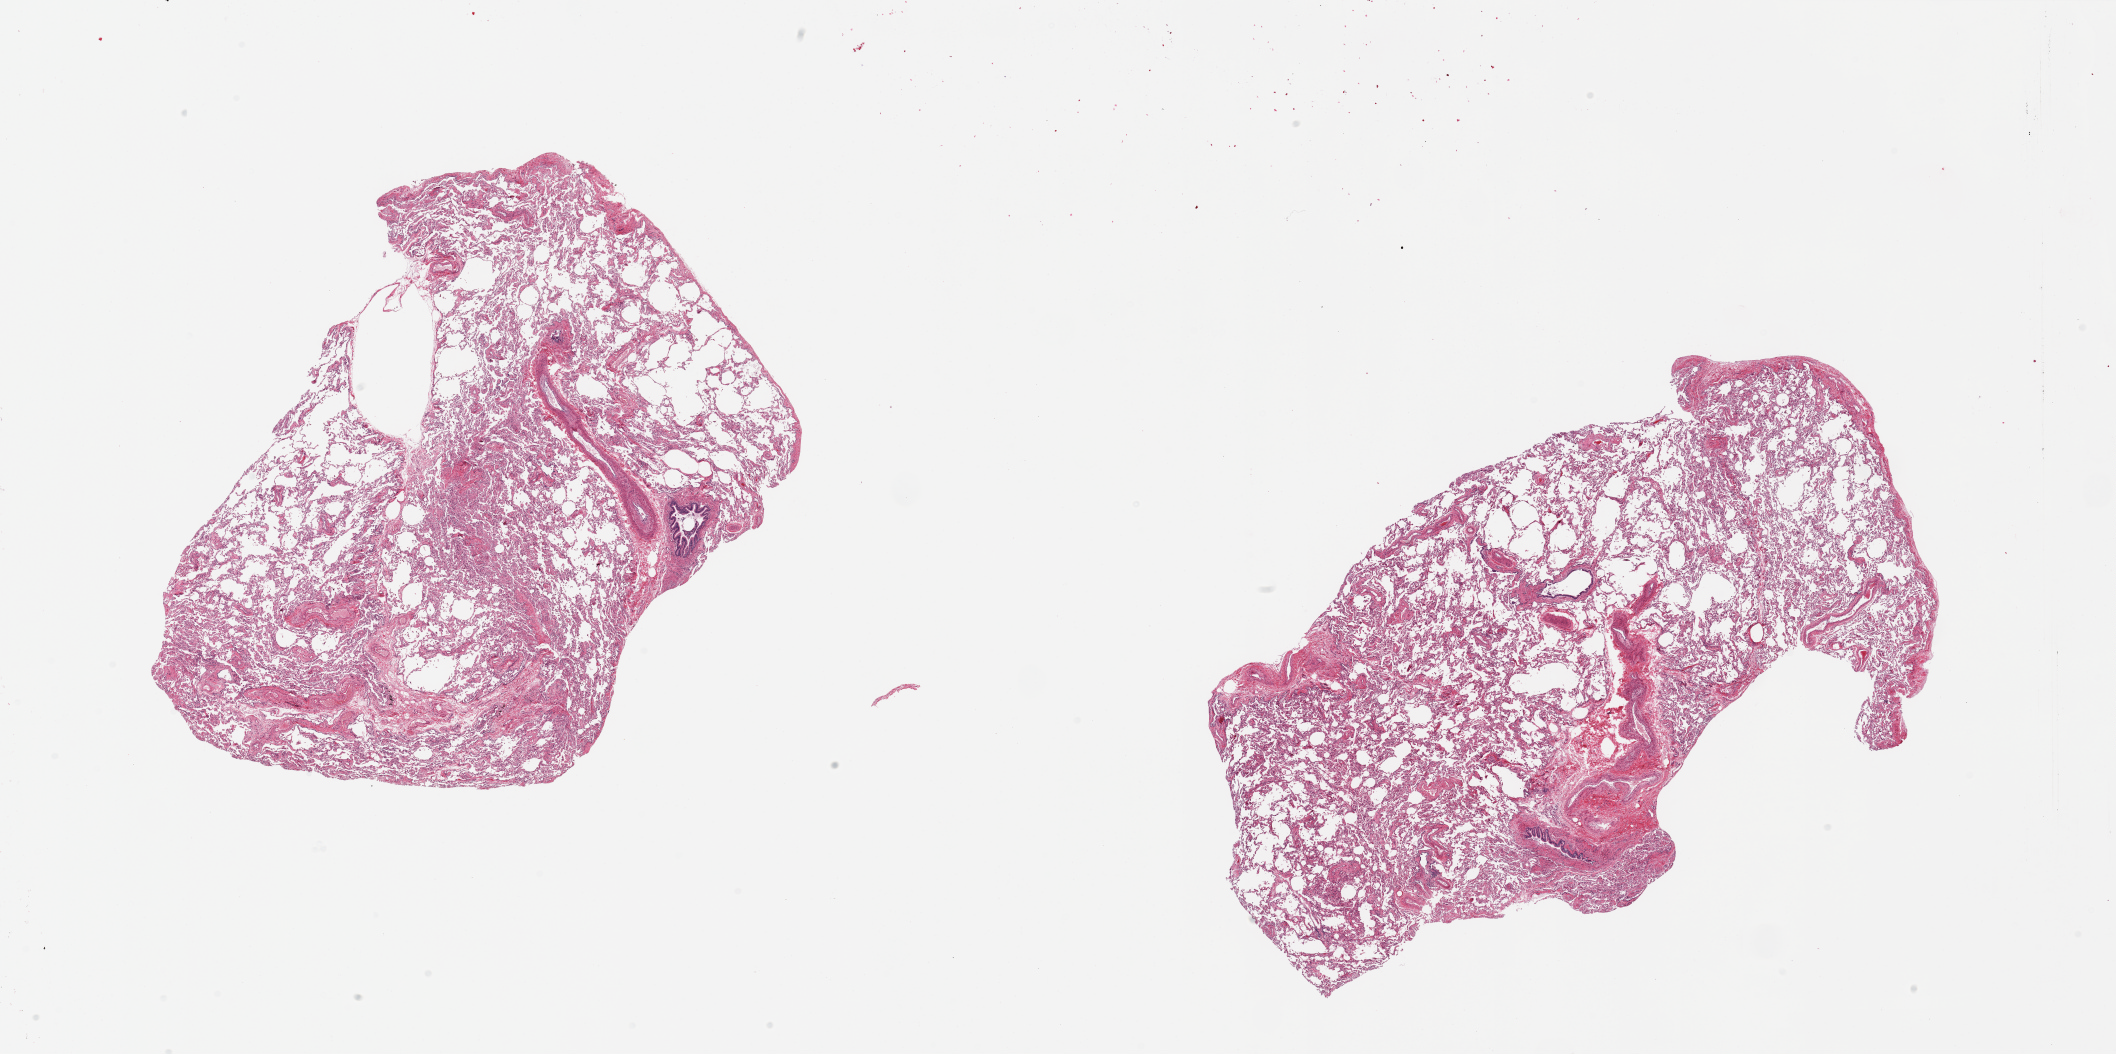
Whole-slide image, haematoxylin and eosin stain, shown as a low-resolution overview of the whole scanned area (about 33.5 x 16.7 mm). PAXgene-fixed paraffin-embedded (PFPE) section. Section of lung (target tissue). Donor tissue sample. Donor sex: male.
Pathologist's review note for this sample: 2 pieces, minimal congestion; rep small bronchioles with well preserved mucosa.